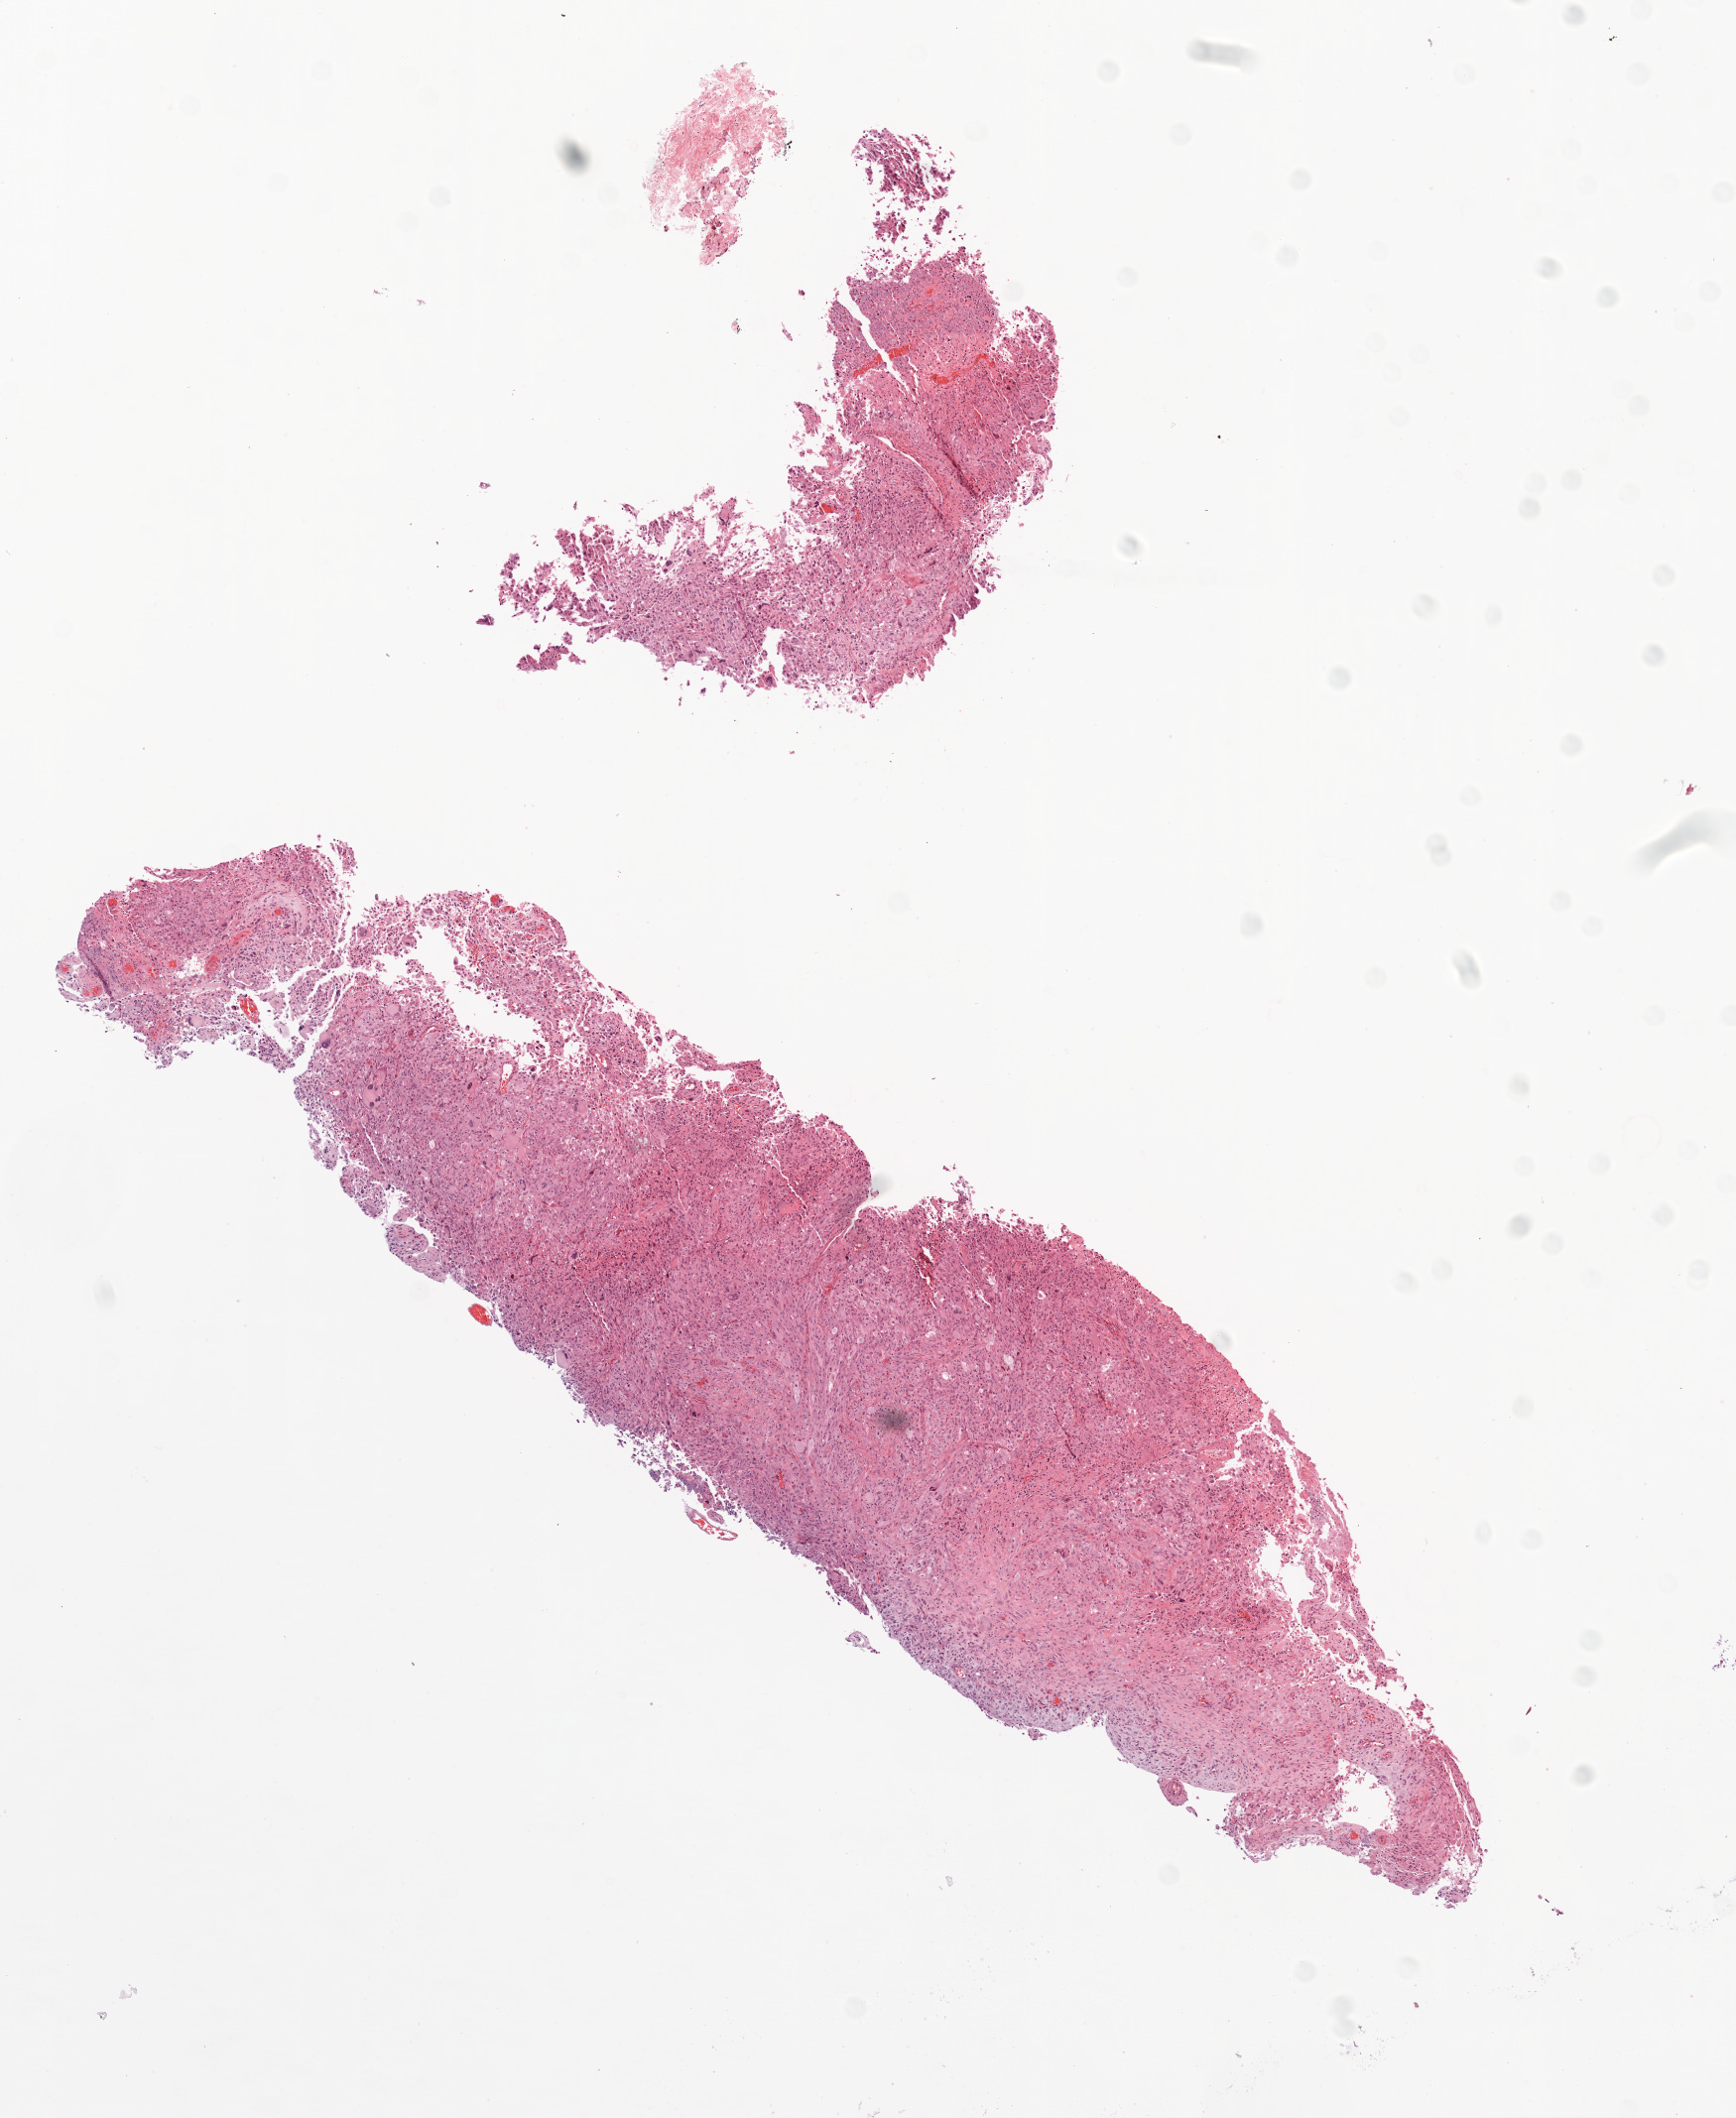
H&E-stained whole-slide image, whole scanned area (about 7.0 x 8.6 mm, from a 20x scan) shown as a low-resolution overview, formalin-fixed paraffin-embedded (FFPE) diagnostic section, primary tumour sample from the brain. Male, age 34 years at initial diagnosis.
* histologic diagnosis: Glioblastoma